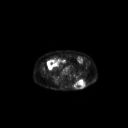
FDG PET of an extremity soft-tissue mass (from a PET/CT study), one axial slice; slice 83 of 267 in the series (ordered by position); 3.27 mm slice thickness; 128 × 128 image matrix, field of view 700 × 700 mm. Male patient, age 69 years. Case-level facts recorded for this patient, not image findings: histological type: leiomyosarcoma; grade: intermediate; site of the primary tumour: left pelvis.
Structures marked on this image (expert contour drawn on MRI and transferred to this co-registered scan by the dataset authors):
- gross tumour volume (mass): box from (x=73, y=78) to (x=86, y=89) px